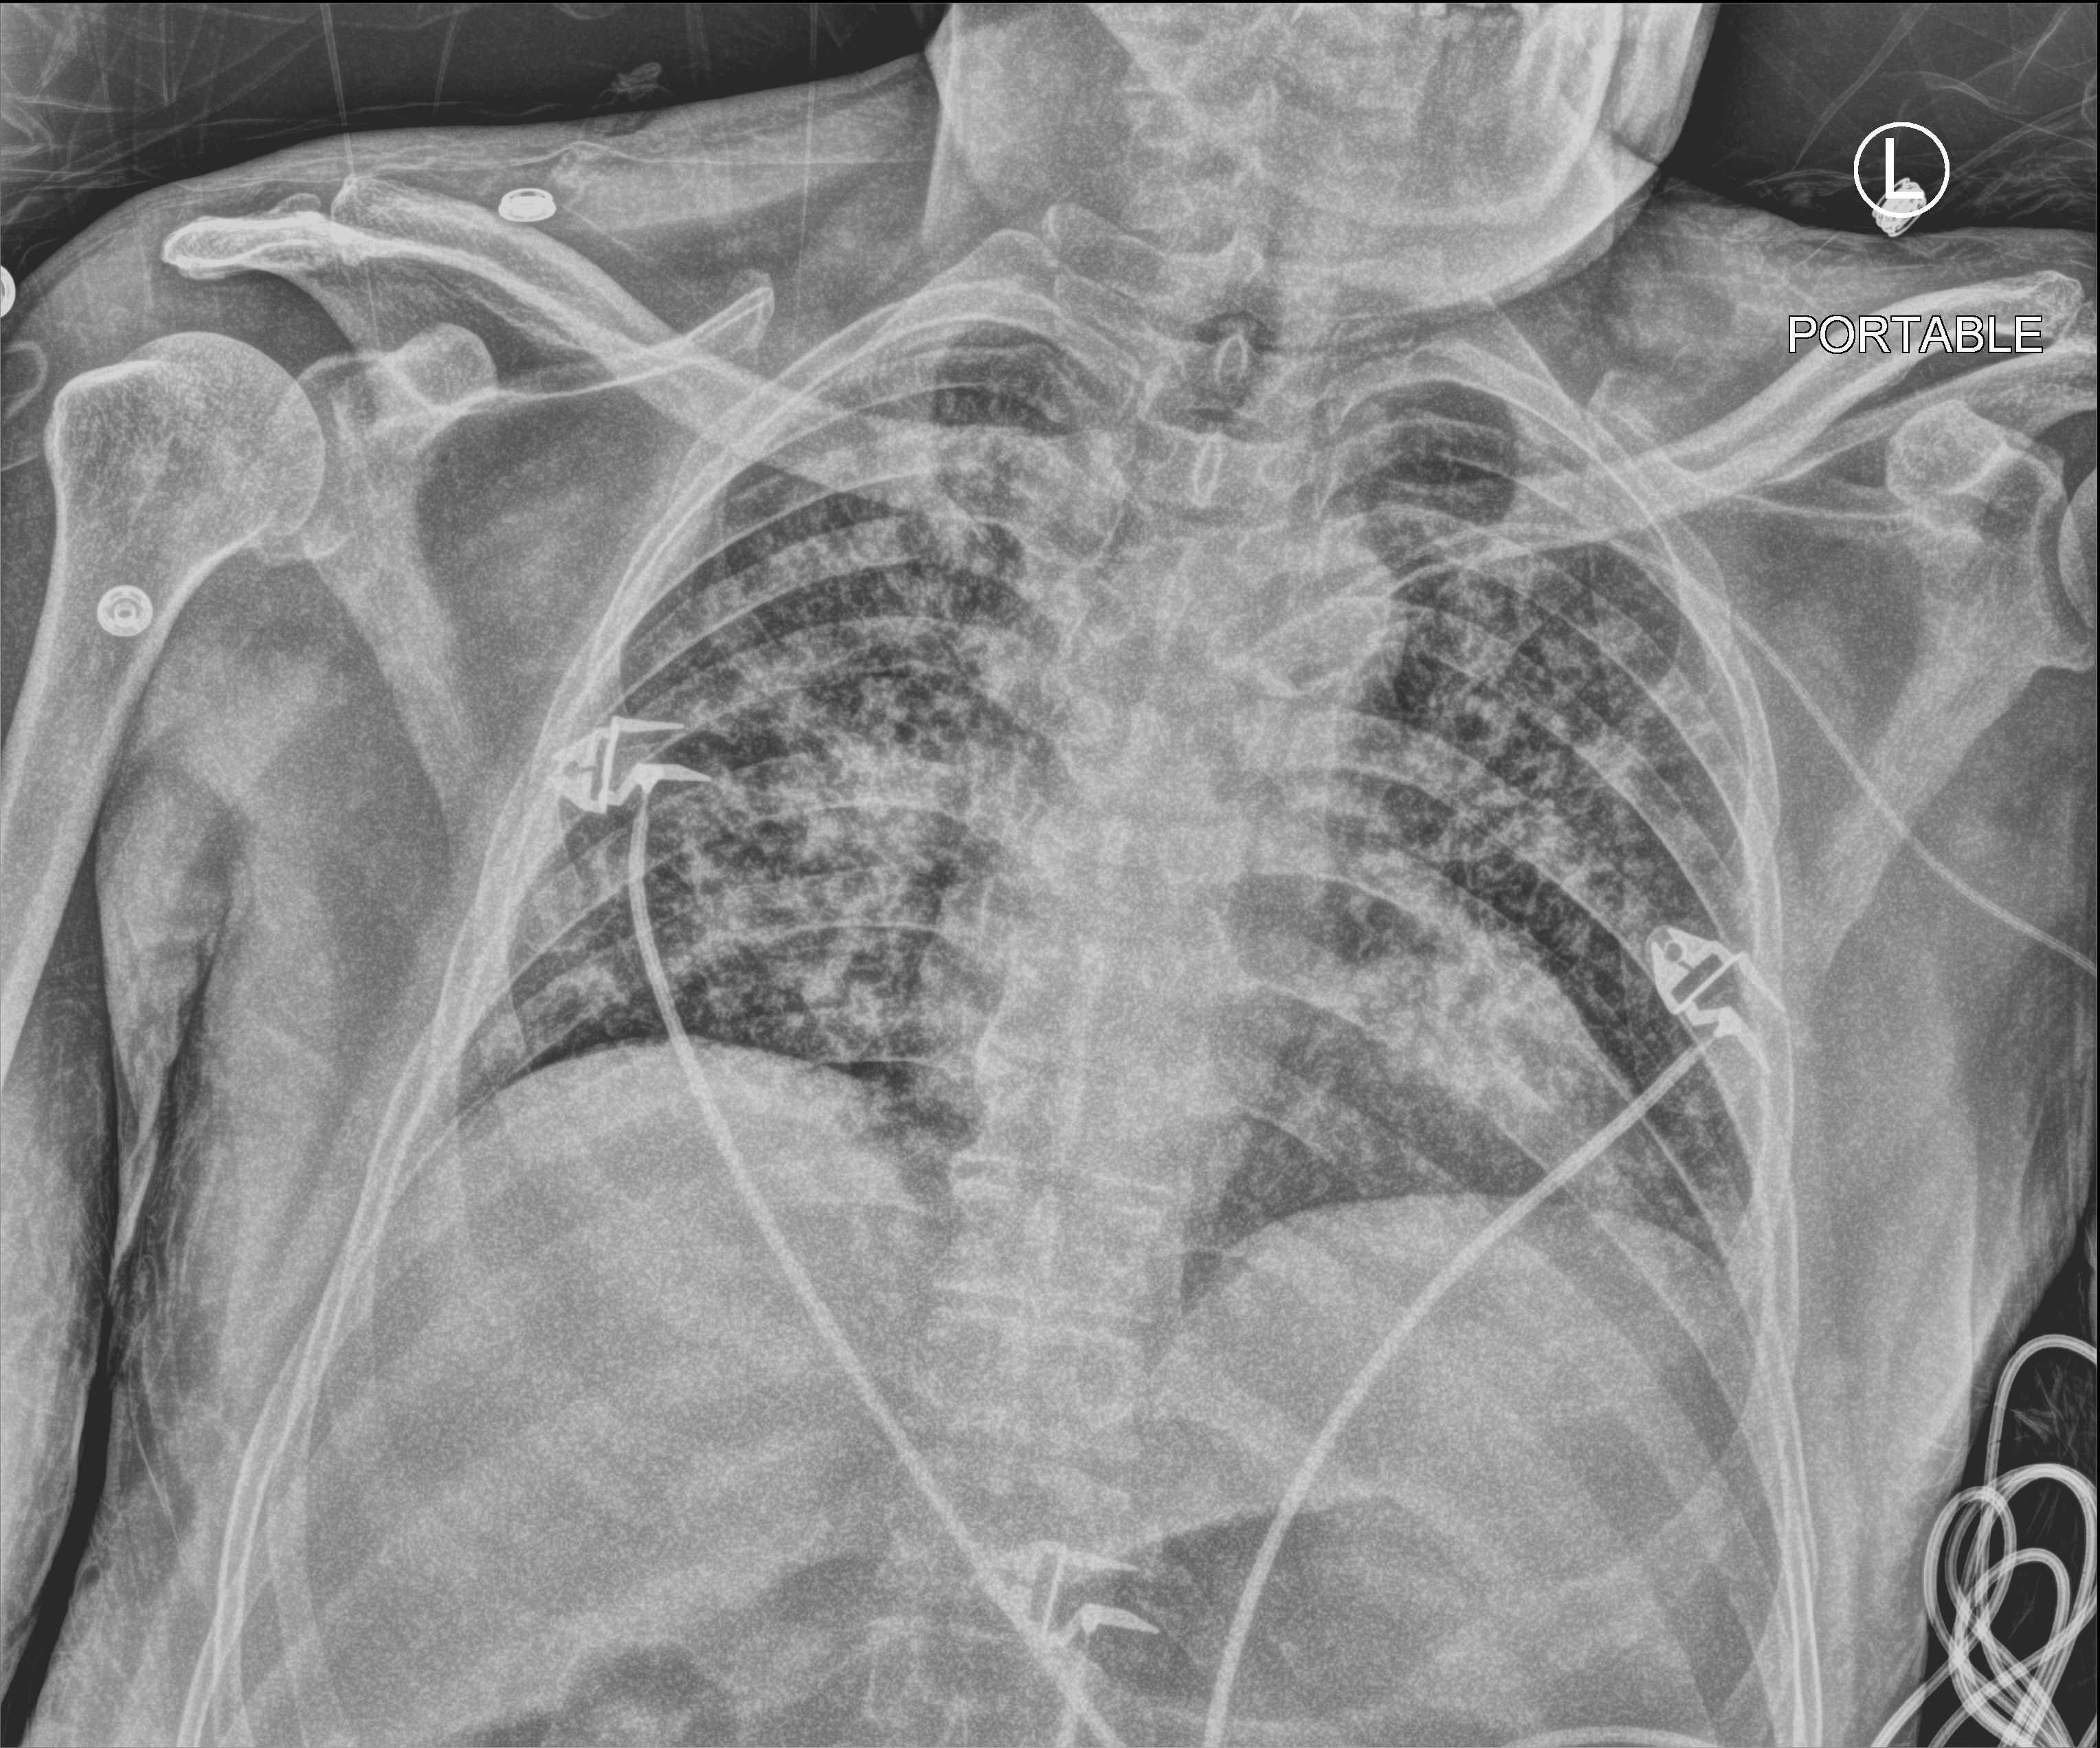
Chest X-ray (portable); anteroposterior (AP) projection. Male patient hospitalised with COVID-19, age 18–59 years.
Hospital-stay facts (about this admission, not read from this image; timing relative to this image not recorded): other chronic lung disease (admission record): no; mechanically ventilated during this hospital stay: yes; admitted to intensive care during this hospital stay: yes.